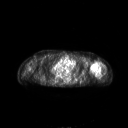
FDG PET of an extremity soft-tissue mass (from a PET/CT study), one axial slice; slice 176 of 267 in the series (ordered by position); 3.27 mm slice thickness; 128 × 128 image matrix, field of view 700 × 700 mm. Patient: female, 83 years. Case-level facts recorded for this patient, not image findings: histological type: pleiomorphic leiomyosarcoma; grade: high; site of the primary tumour: left biceps.
Annotated regions visible in this slice (expert contour drawn on MRI and transferred to this co-registered scan by the dataset authors):
- gross tumour volume including surrounding oedema: bounding box <90,60,102,77> (left, top, right, bottom; pixels)
- gross tumour volume (mass): <90,60,102,74>